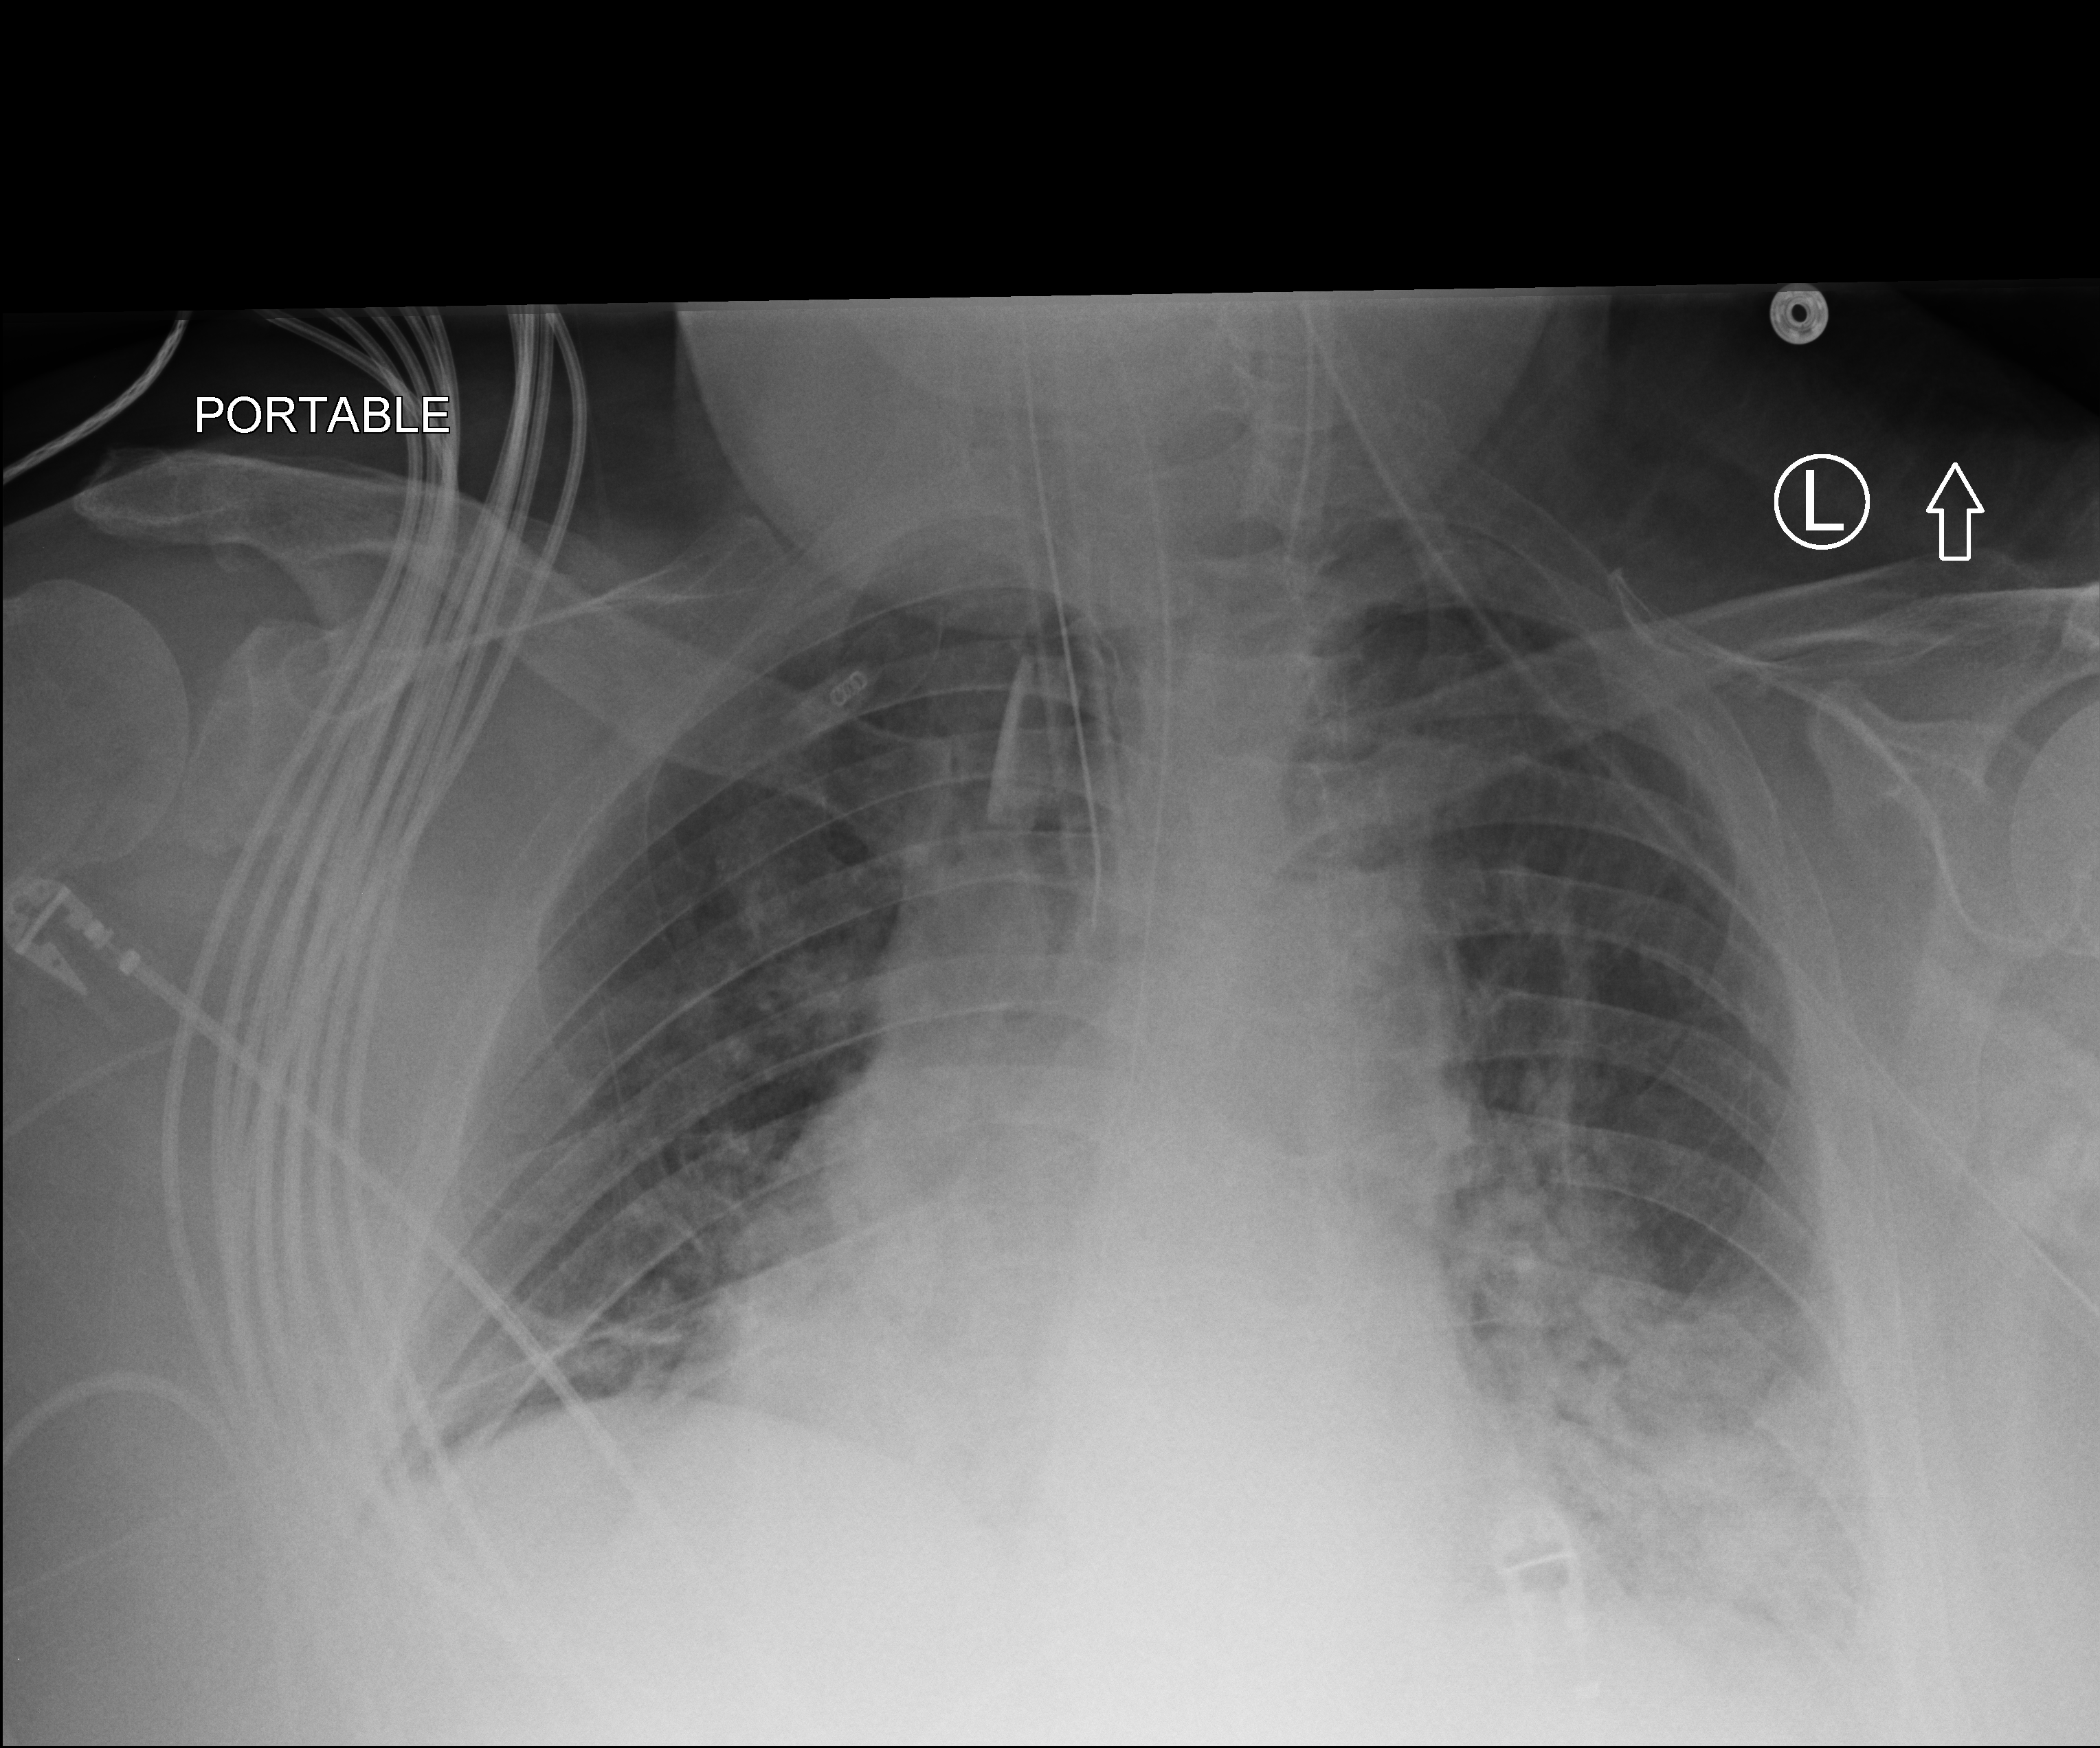
Portable chest radiograph; anteroposterior (AP) projection. Male patient hospitalised with COVID-19, age 60–74 years.
Hospital-stay facts (about this admission, not read from this image; timing relative to this image not recorded): admitted to intensive care during this hospital stay: yes; mechanically ventilated during this hospital stay: yes.